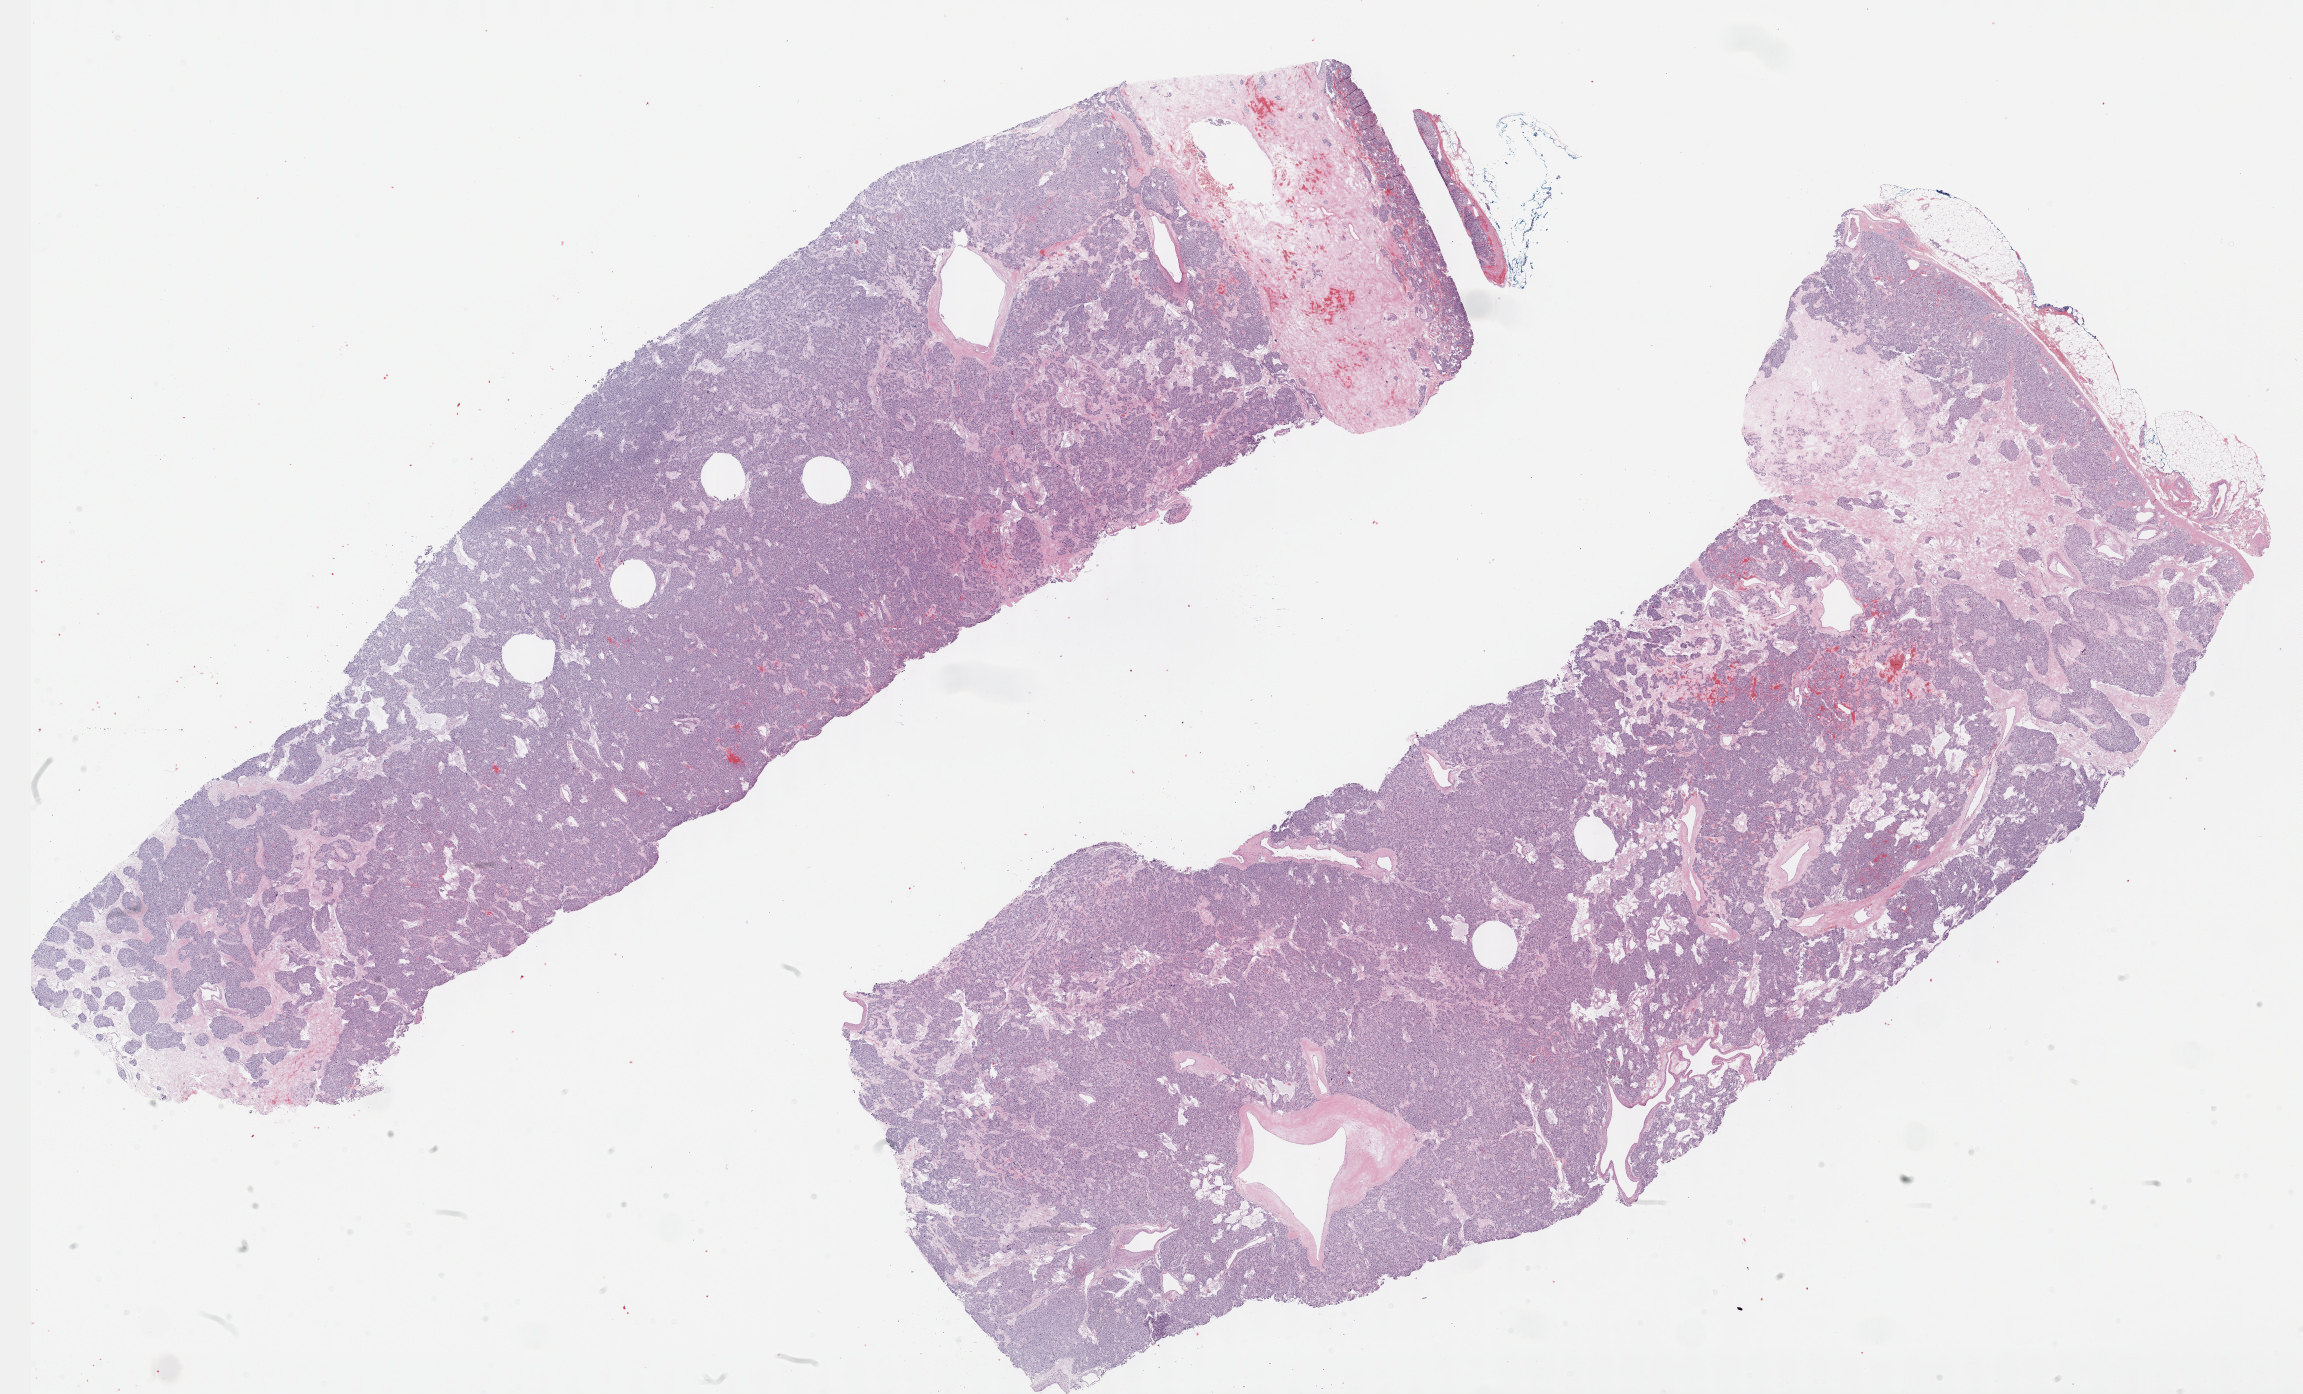
H&E-stained whole-slide image — a low-resolution overview of the entire scanned area, about 37.2 x 22.5 mm (from a 40x scan); formalin-fixed paraffin-embedded (FFPE) diagnostic section; sample: primary tumour, adrenal gland. Male patient; age at initial diagnosis 47 years.
Laterality: left. Histologic diagnosis: Pheochromocytoma, malignant. Lymph nodes positive (case pathology): 0 of 1 examined.